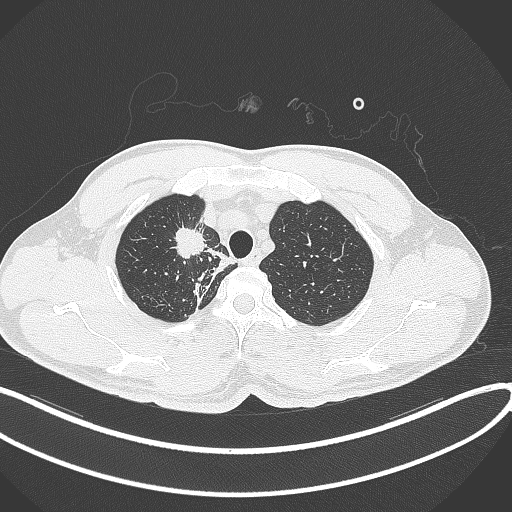
Chest CT, one axial slice. Position 318 of 391 along the scan axis. Lung window (W 1500 / L -600 HU). 1 mm slice thickness. 512 × 512 image matrix. Patient: male, 48 years. From the clinical record (not read from this slice): clinical TNM (as recorded): T1c N1 M1.
Annotated regions visible in this slice (bounding box drawn by a radiologist):
- lung tumour (recorded histology: adenocarcinoma): bounding box (x1, y1, x2, y2) in pixels: (173, 221, 210, 260)